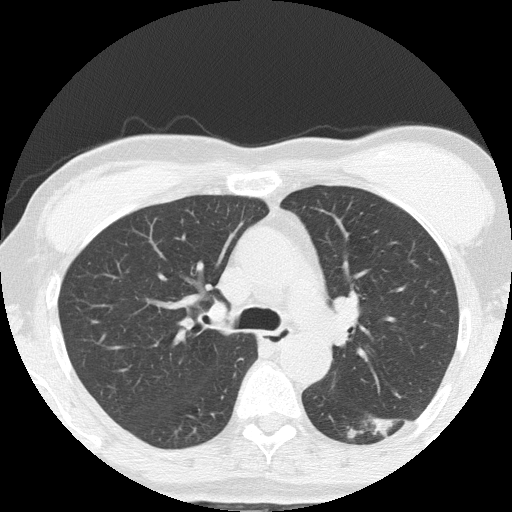
Low-dose screening chest CT, axial slice; third screening round (two years after baseline); lung window (W 1500 / L -600 HU); 2 mm slice thickness; 120 kVp. Female participant, aged 64 years at enrolment. Former smoker at enrolment.
Expert-annotated lung lesion, bounding box <341,392,427,459> (left, top, right, bottom; pixels). The screening reader recorded 3 non-calcified nodules or masses ≥4 mm on this exam (right upper lobe, left lower lobe, right middle lobe); which of them this box marks is not recorded.